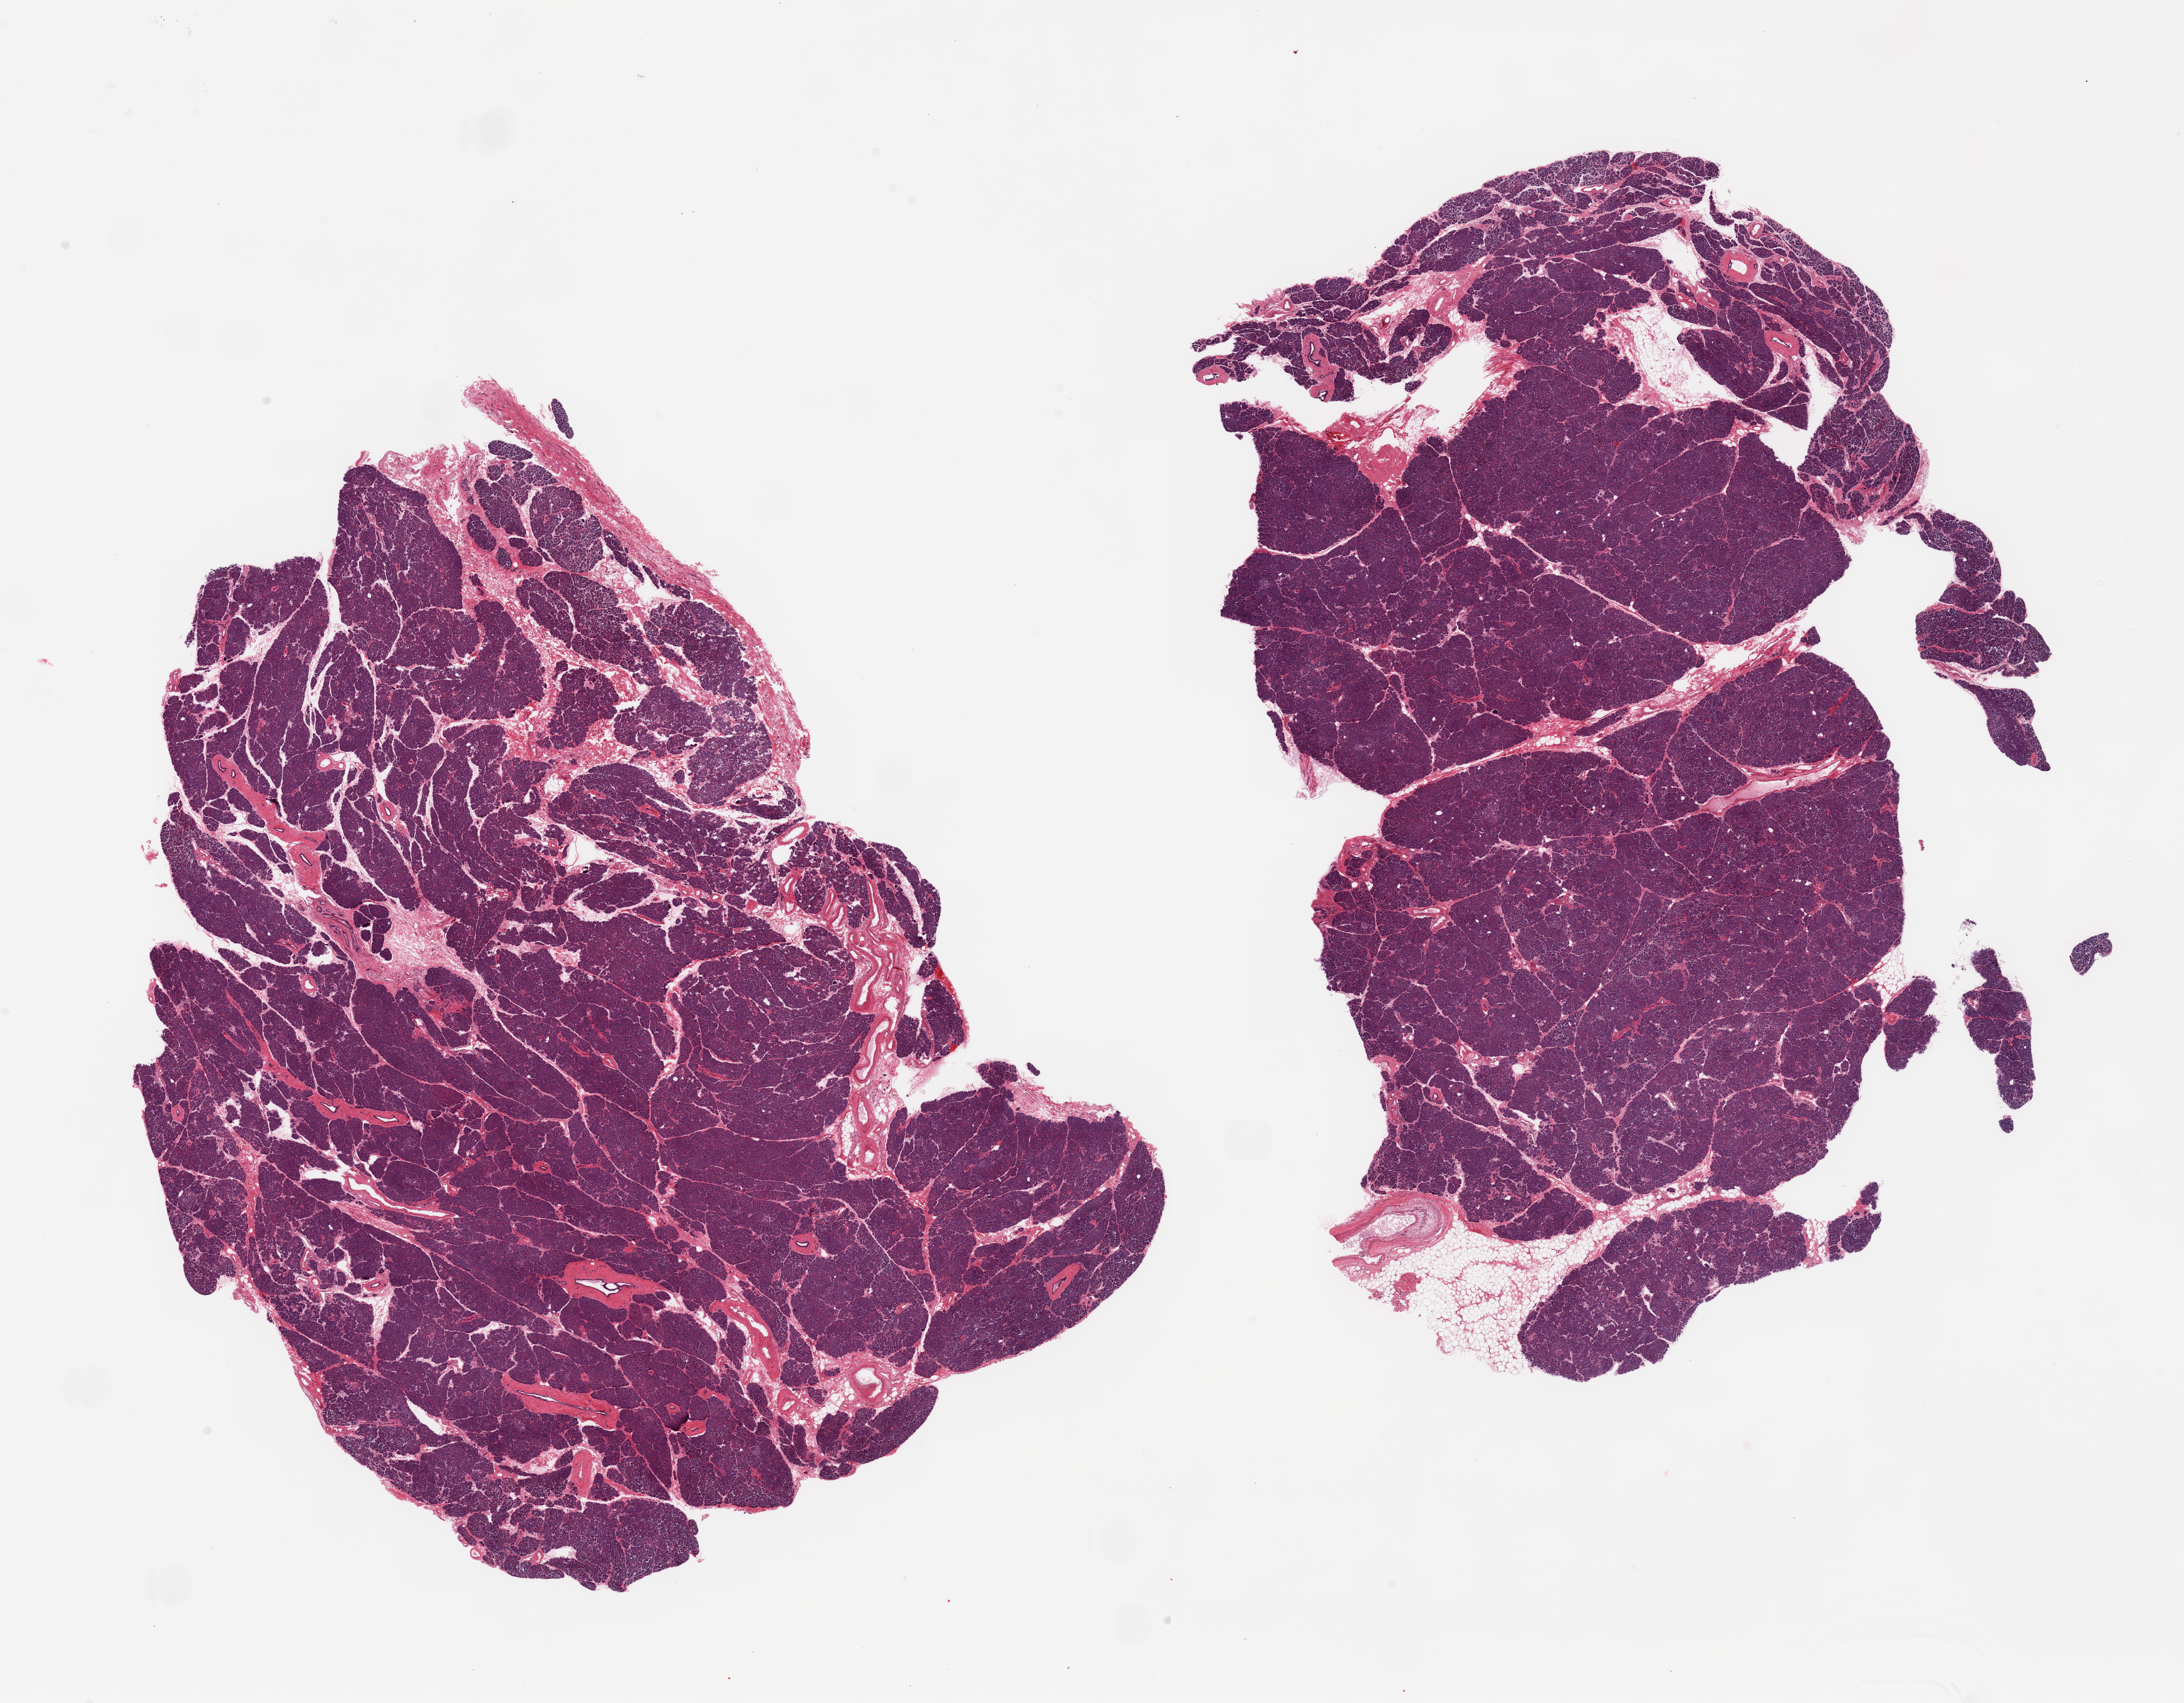
Digitized H&E-stained section, shown as a low-resolution overview of the whole scanned area (about 27.6 x 21.5 mm); PAXgene-fixed, paraffin-embedded tissue; target tissue: pancreas; tissue donor sample. Donor sex: female.
Reviewer comment on this tissue sample: 2 pieces, centrally approaching score 2 for autolysis; Islets fairly well preserved, but rare.